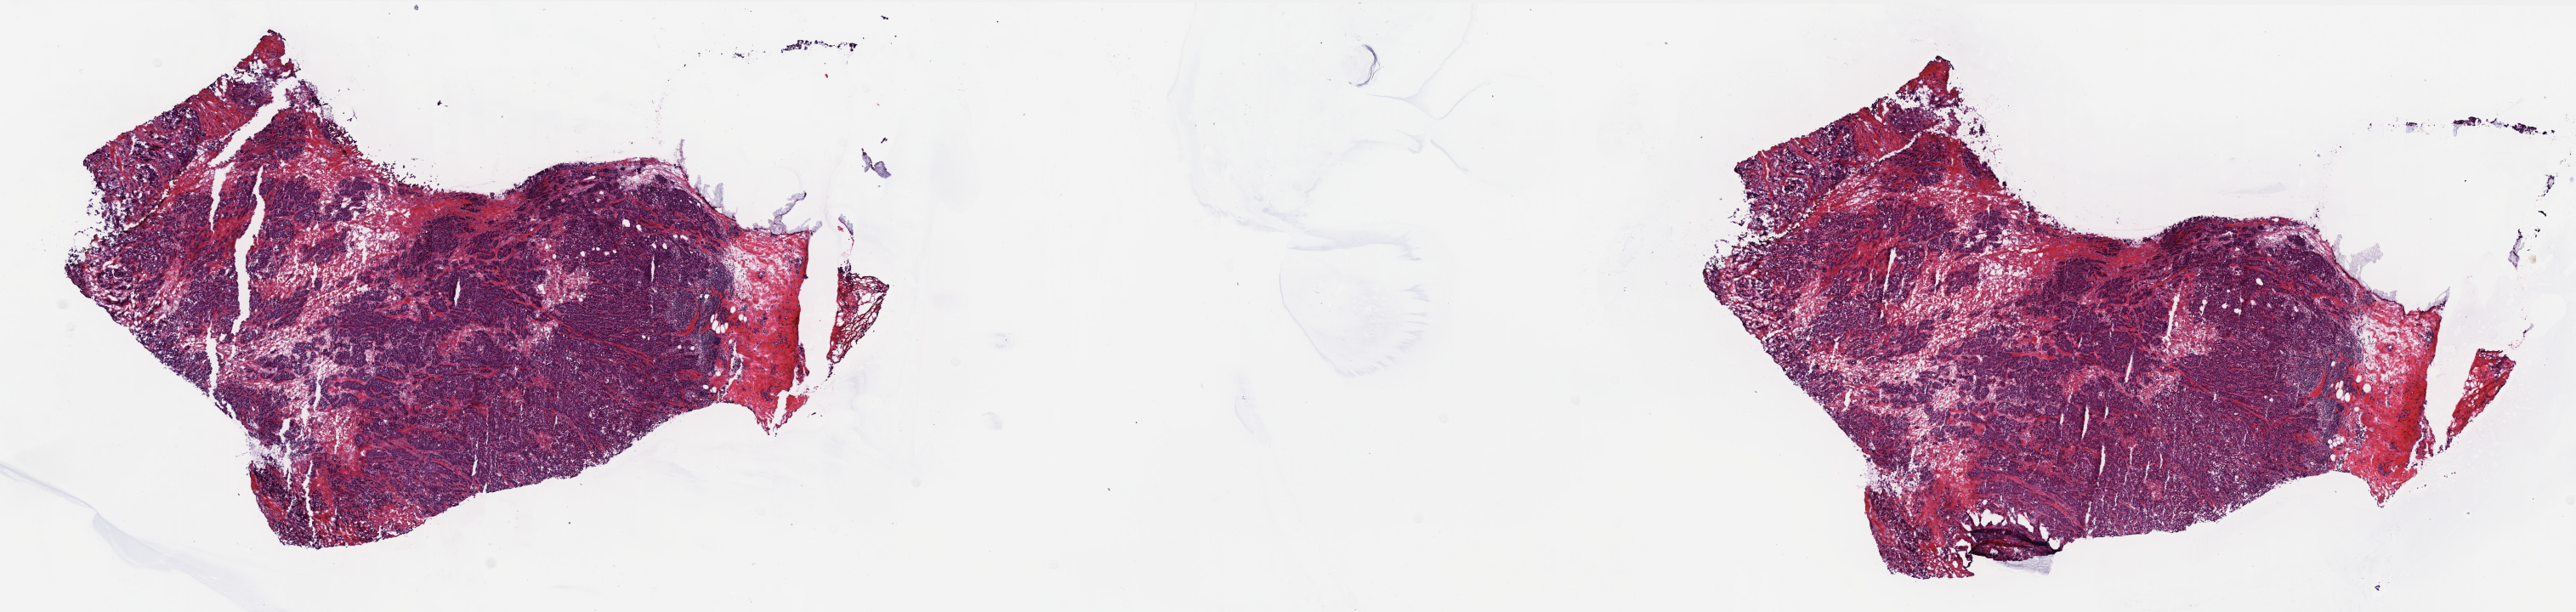
Whole-slide histology image, H&E-stained, a low-resolution overview of the entire scanned area, about 24.3 x 5.8 mm; frozen section from the top of the tissue portion; breast, primary tumour sample. Patient: female, age at initial diagnosis 57 years. Pathologist review of this section (percent, as recorded): tumour cells 78%, tumour nuclei 80%, normal cells 0%, stromal cells 17%, necrosis 5%. Inflammatory infiltration, as recorded: lymphocyte infiltration 9%, monocyte infiltration 0%, neutrophil infiltration 0%.
* TNM: T2 N0 (i-) M0
* AJCC pathologic stage: IIA
* diagnosis: Infiltrating duct carcinoma, NOS
* lymph nodes positive (case pathology): 0 of 1 examined